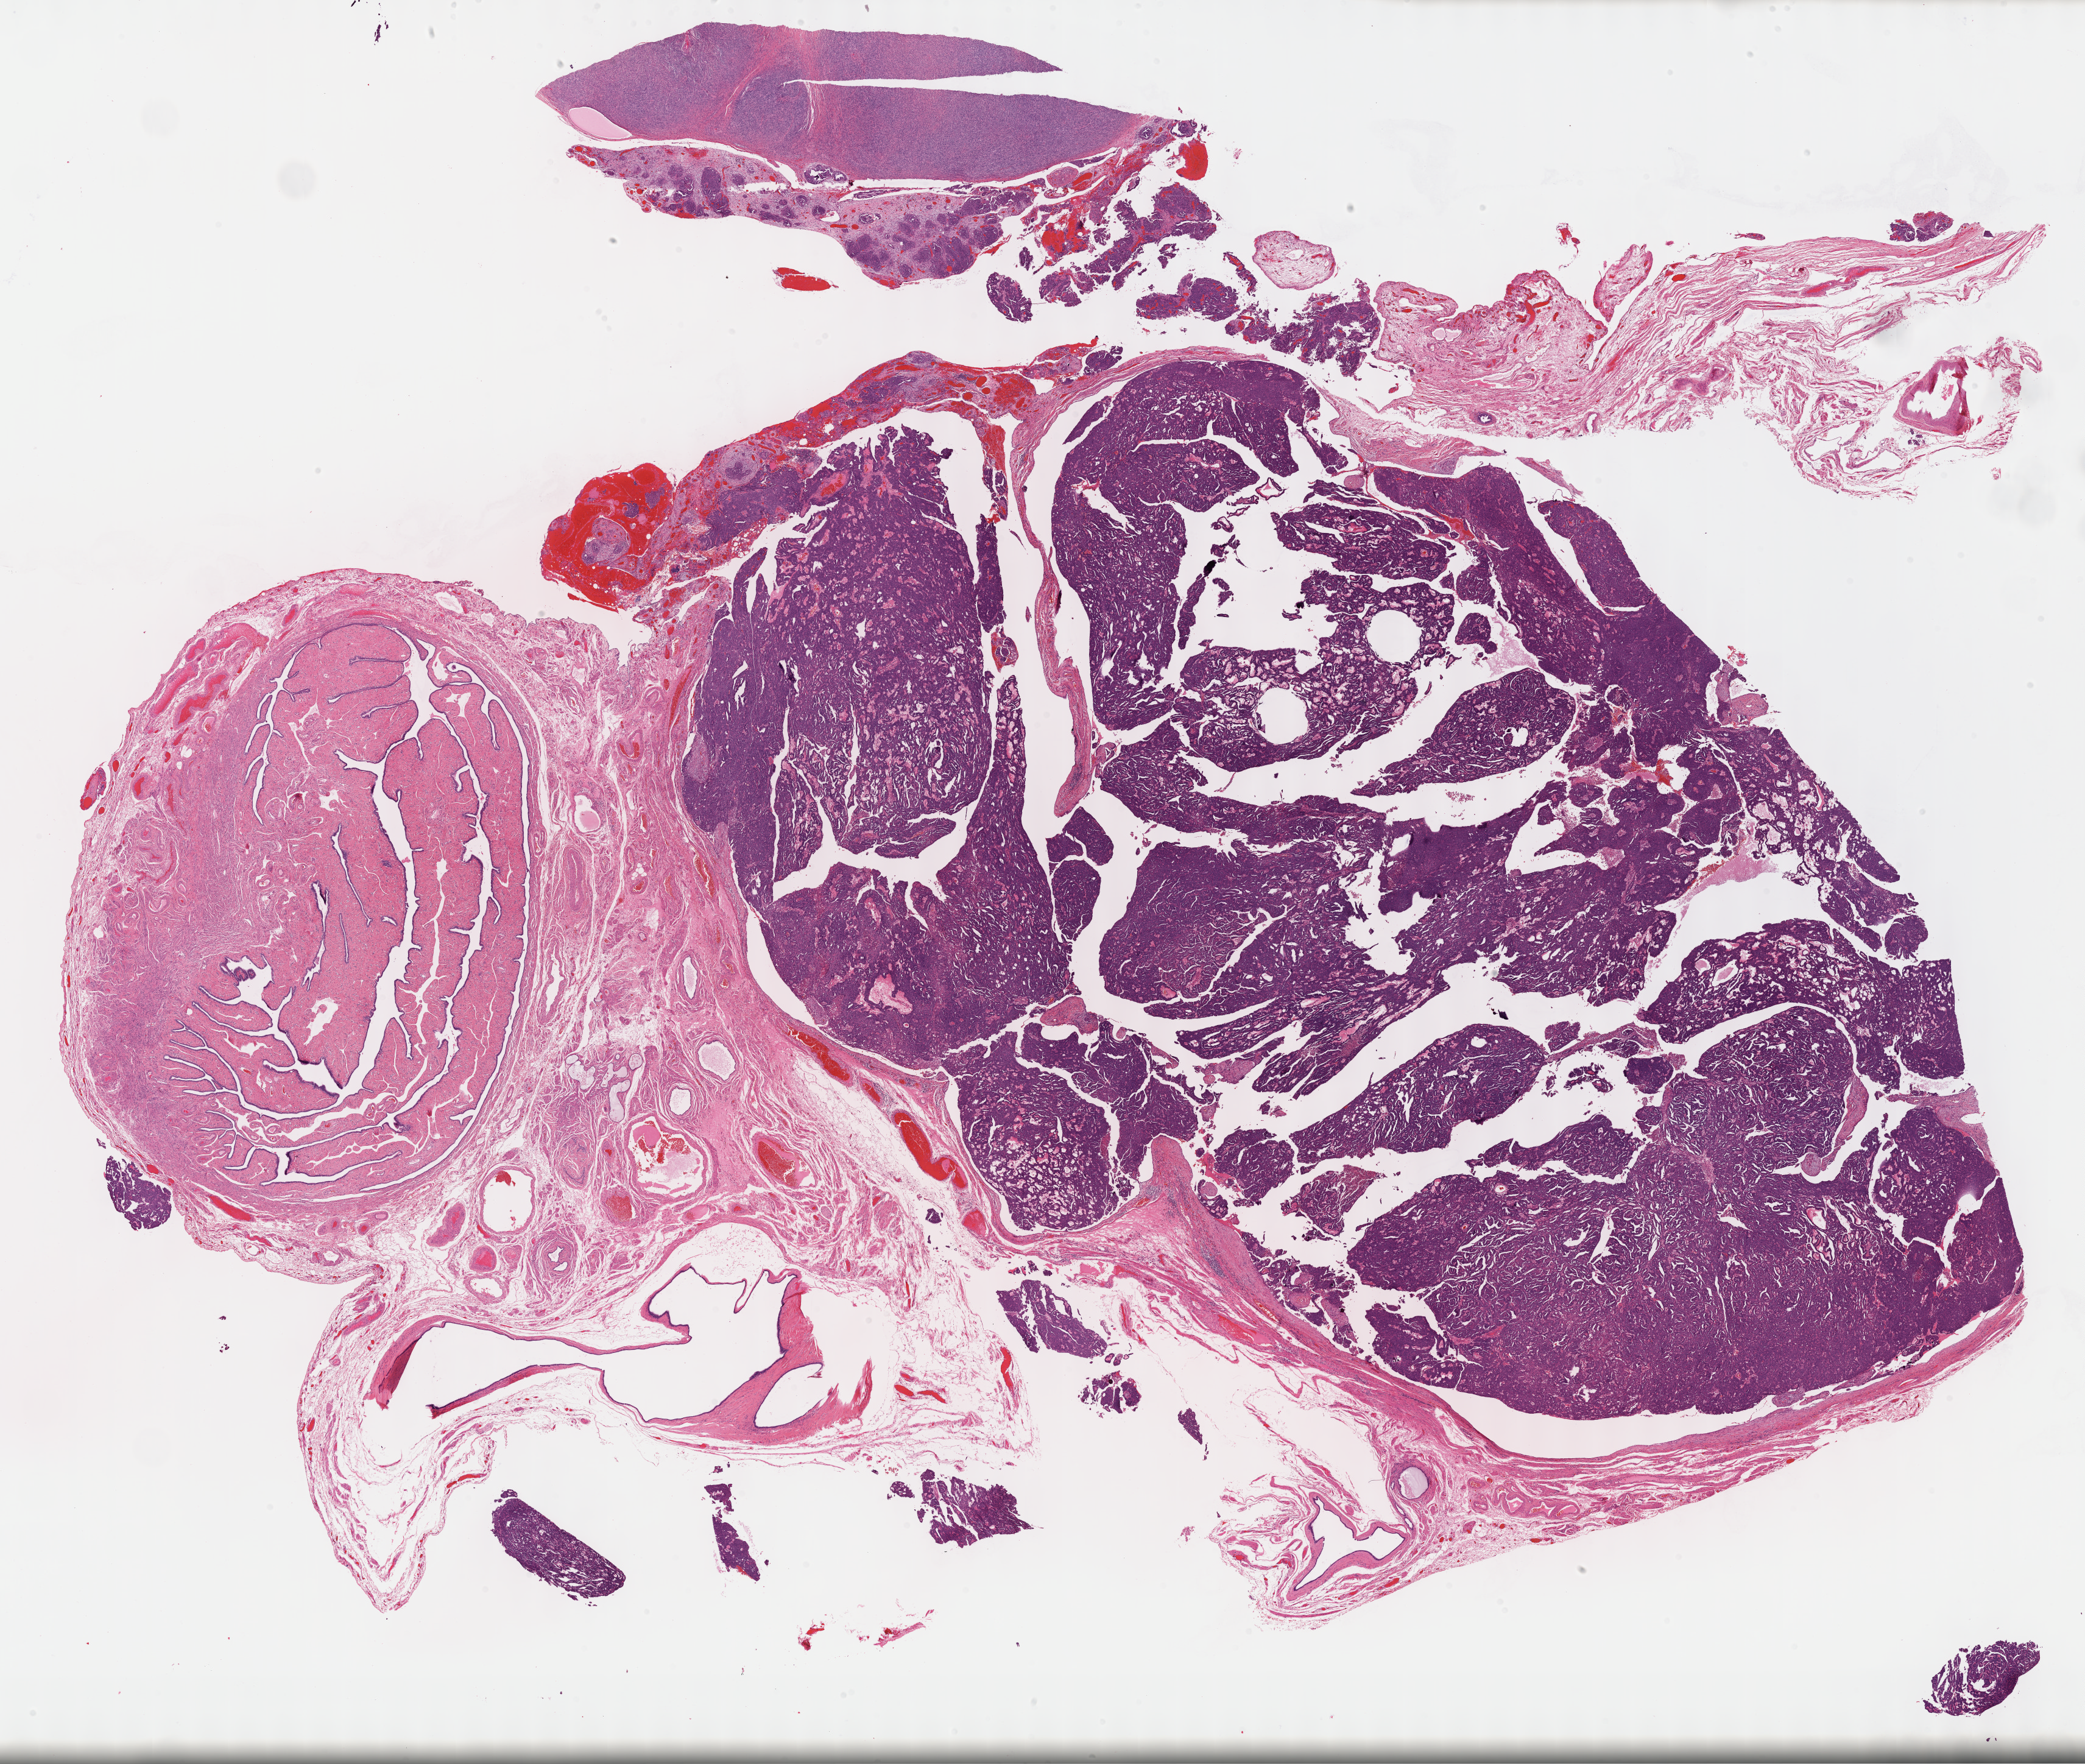
H&E whole-slide image — low-resolution overview of the scanned area, about 27.7 x 23.4 mm (from a 40x scan). FFPE section. Sample: primary tumour, ovary. Female, age 64 years at initial diagnosis. Histologic grade: G3 (poorly differentiated).
Laterality: left. FIGO stage: IIIC. Diagnosis: Serous cystadenocarcinoma, NOS.